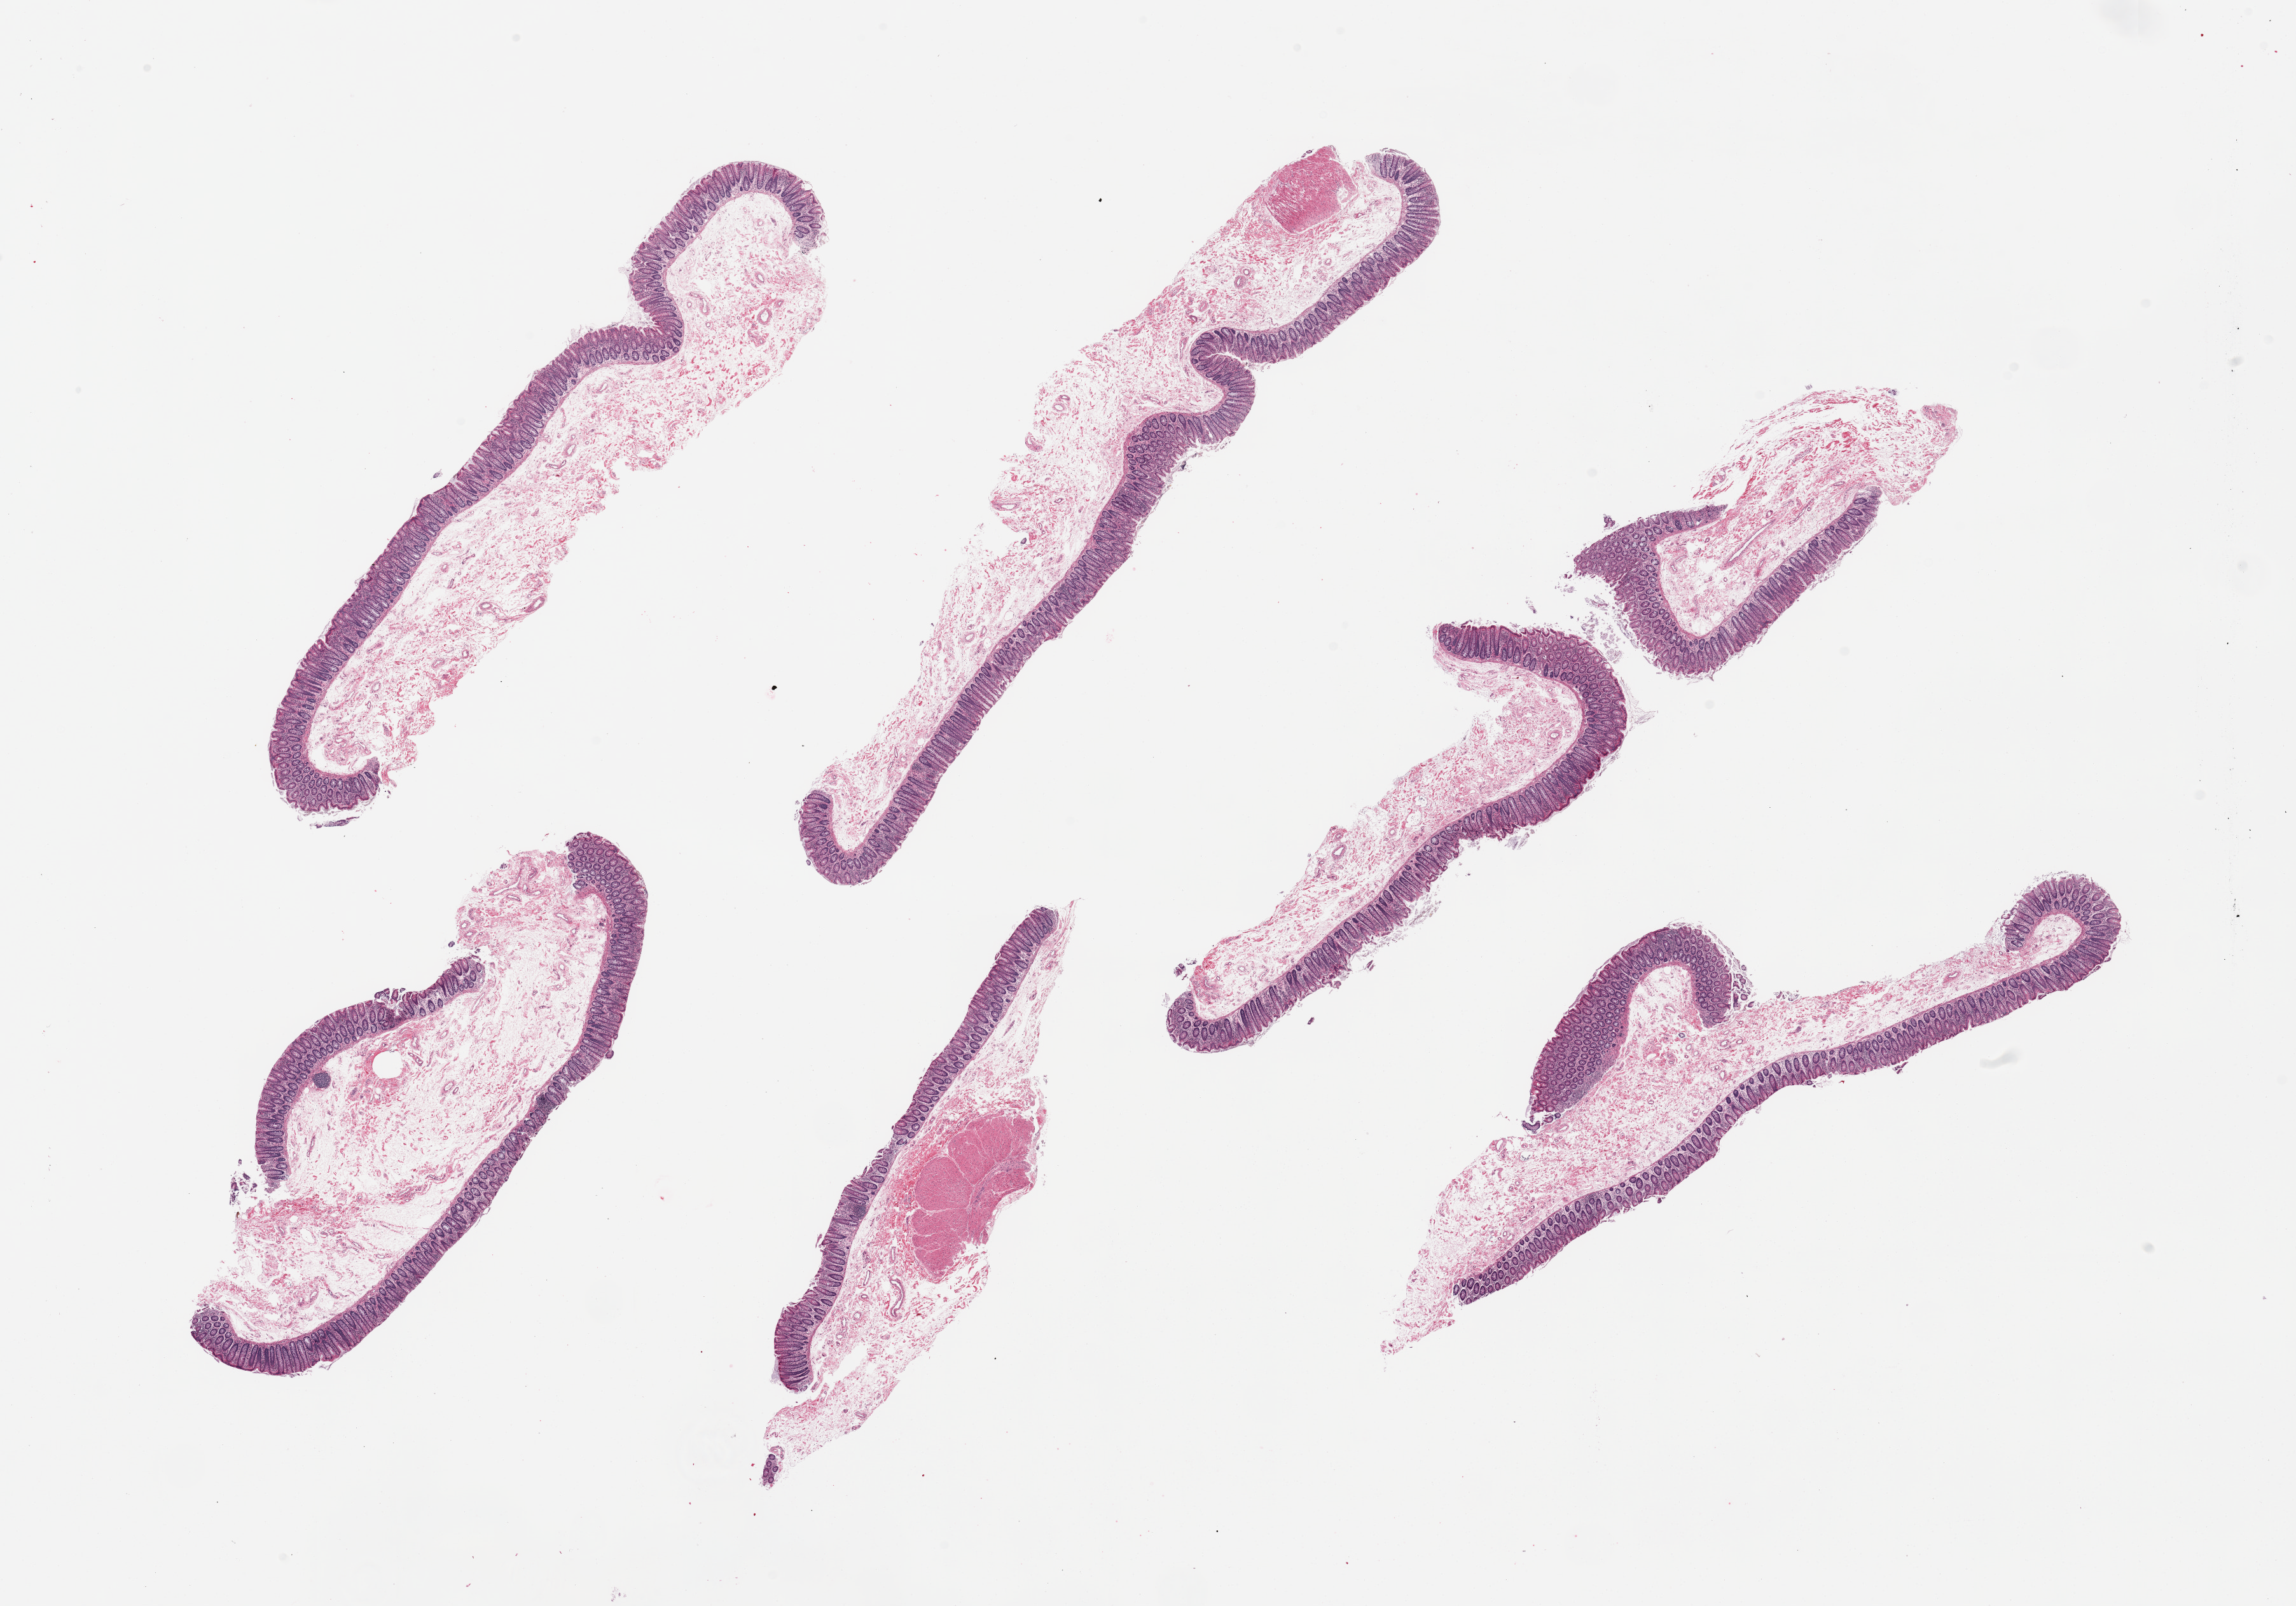
Hematoxylin and eosin (H&E) whole-slide image — whole scanned area (about 28.5 x 20.0 mm, from a 20x scan) shown as a low-resolution overview. PAXgene-fixed paraffin-embedded (PFPE) section. Section of transverse colon (target tissue). Donor tissue sample. Donor sex: male.
Reviewer comment on this tissue sample: 6 pieces; predominantly mucosa/submucosa, 2 with small portion of muscularis.